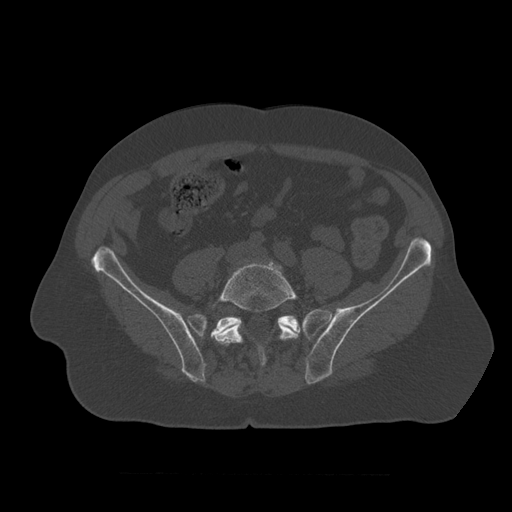
CT including the spine, one axial slice; position 250 of 450 along the scan axis; reconstruction kernel STANDARD; bone window (W 1800 / L 400 HU); 1.25 mm slice thickness; 512 × 512 image matrix, field of view 405 × 405 mm. Patient age 75 years. From the clinical record (not read from this slice): primary cancer: prostate.
Structures marked on this image (semi-automatically segmented with operator editing):
- L5 vertebra: box from (x=213, y=261) to (x=299, y=366) px